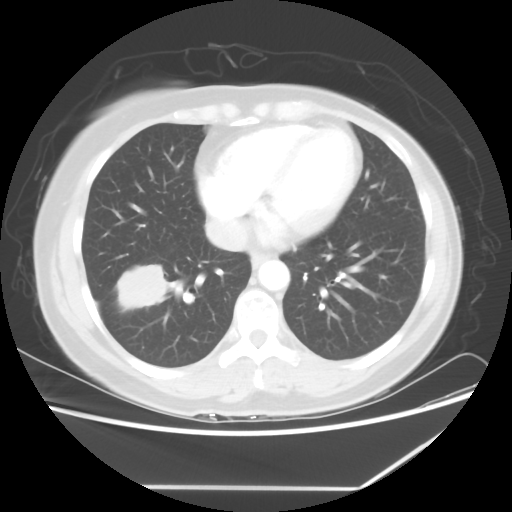
Chest CT, one axial slice. Slice 23 of 60 in the series (ordered by position). 100 kVp. Lung window (W 1500 / L -600 HU). 512 × 512 image matrix, field of view 374 × 374 mm. Patient: female, 42 years. Case-level facts recorded for this patient, not image findings: clinical TNM (as recorded): T2 N1 M0.
Structures marked on this image (bounding box drawn by a radiologist):
- lung tumour (recorded histology: adenocarcinoma): bounding box <112,253,168,319> (left, top, right, bottom; pixels)